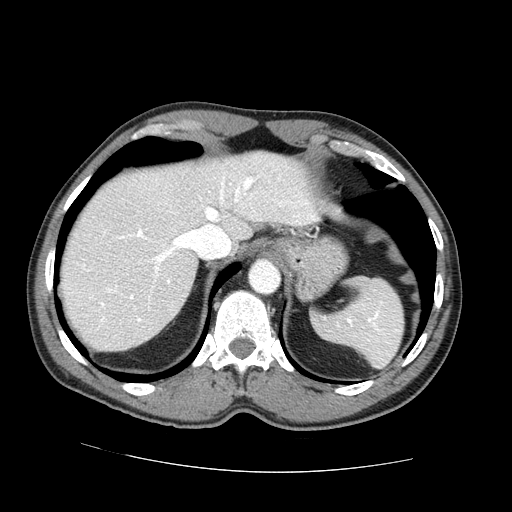
Contrast-enhanced abdominal CT (liver protocol), one axial slice. Position 57 of 73 along the scan axis. Reconstruction kernel STANDARD. One of 2 acquisitions stored at this slice position. Soft-tissue window (W 400 / L 40 HU). 2.5 mm slice thickness. 512 × 512 image matrix, field of view 380 × 380 mm. Case-level facts recorded for this patient, not image findings: diagnosis: hepatocellular carcinoma (patient treated with transarterial chemoembolisation; whether this scan precedes or follows treatment is not stated here); TNM stage (as recorded): Stage-IVA; Child-Pugh class: A; tumour differentiation: no biopsy; tumour nodularity: uninodular.
Structures marked on this image (semi-automatically segmented with operator editing):
- abdominal aorta: bounding box (x1, y1, x2, y2) in pixels: (250, 260, 280, 293)
- liver parenchyma outside the tumour (the mass and vessels are separate outlines, so this box may not span the whole liver): (60, 152, 318, 350)
- liver vessels: (101, 176, 313, 322)